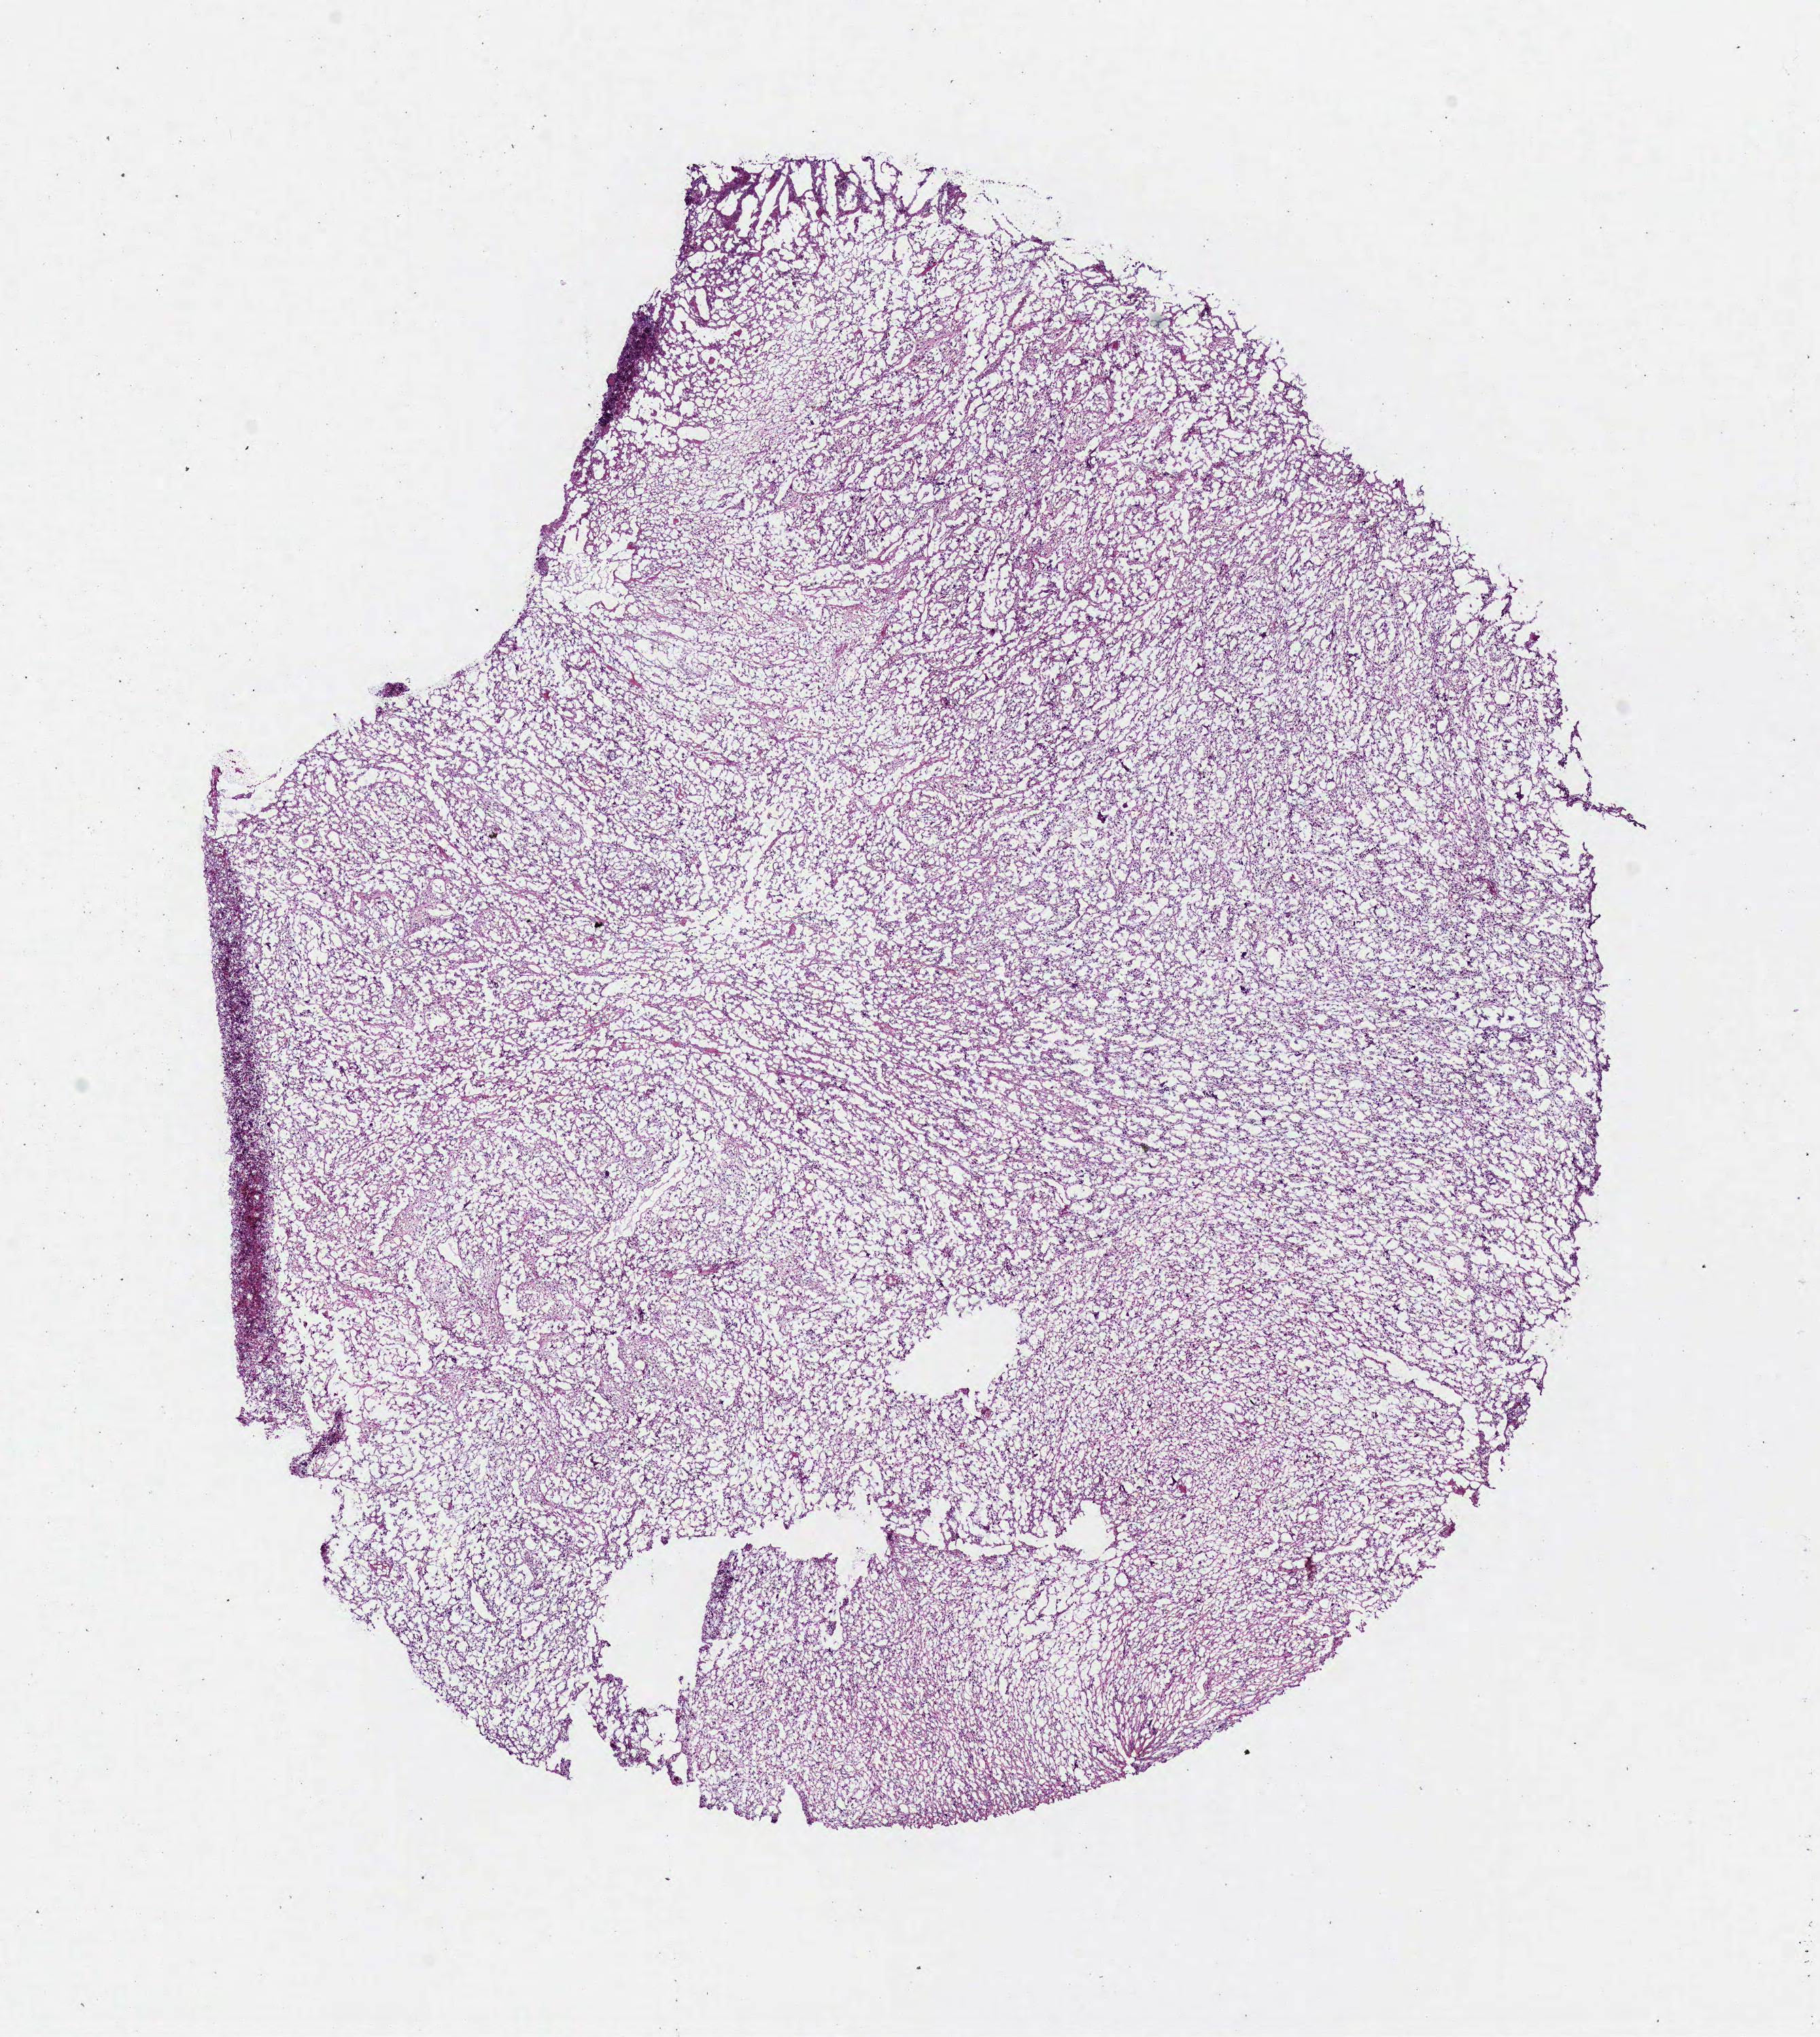
Digitized H&E-stained tissue section (whole slide) — a low-resolution overview of the entire scanned area, about 10.5 x 11.8 mm (slide scanned at 40x), frozen section from the bottom of the tissue portion, brain, primary tumour sample. Patient: female, age at initial diagnosis 47 years. Composition of this section per pathologist review: tumour cells 100%, tumour nuclei 75%, normal cells 0%, stromal cells 0%, necrosis 0%.
• diagnosis: Glioblastoma